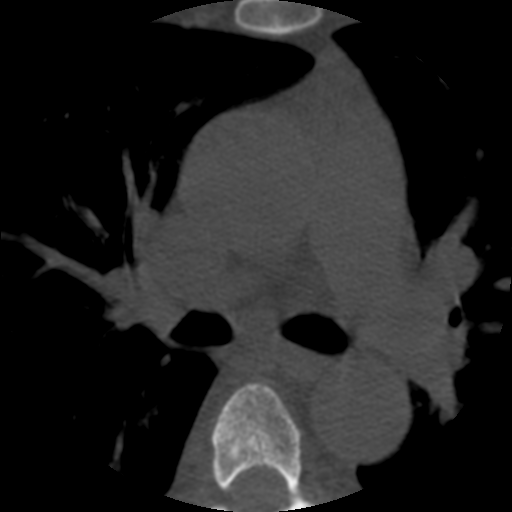
CT including the spine, one axial slice. Slice 375 of 508 in the series (ordered by position). Reconstruction kernel STANDARD. Bone window (W 1800 / L 400 HU). 1.25 mm slice thickness. 512 × 512 image matrix, field of view 160 × 160 mm. Patient age 57 years. Case-level facts recorded for this patient, not image findings: primary cancer: prostate.
Outlined on this slice (semi-automatically segmented with operator editing):
- T5 vertebra: bounding box [x1, y1, x2, y2] px = [211, 383, 317, 512]
- T6 vertebra: [212, 505, 227, 512]